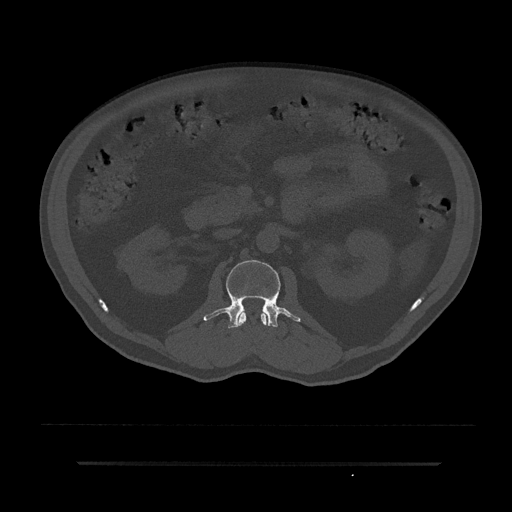
CT including the spine, one axial slice; position 93 of 797 along the scan axis; bone window (W 1800 / L 400 HU); 0.5 mm slice thickness; 512 × 512 image matrix. Male patient, age 59 years. From the clinical record (not read from this slice): primary cancer: bile ducts.
Annotated regions visible in this slice (semi-automatically segmented with operator editing):
- L1 vertebra: bounding box [x1, y1, x2, y2] px = [238, 311, 267, 326]
- L2 vertebra: [203, 260, 301, 329]